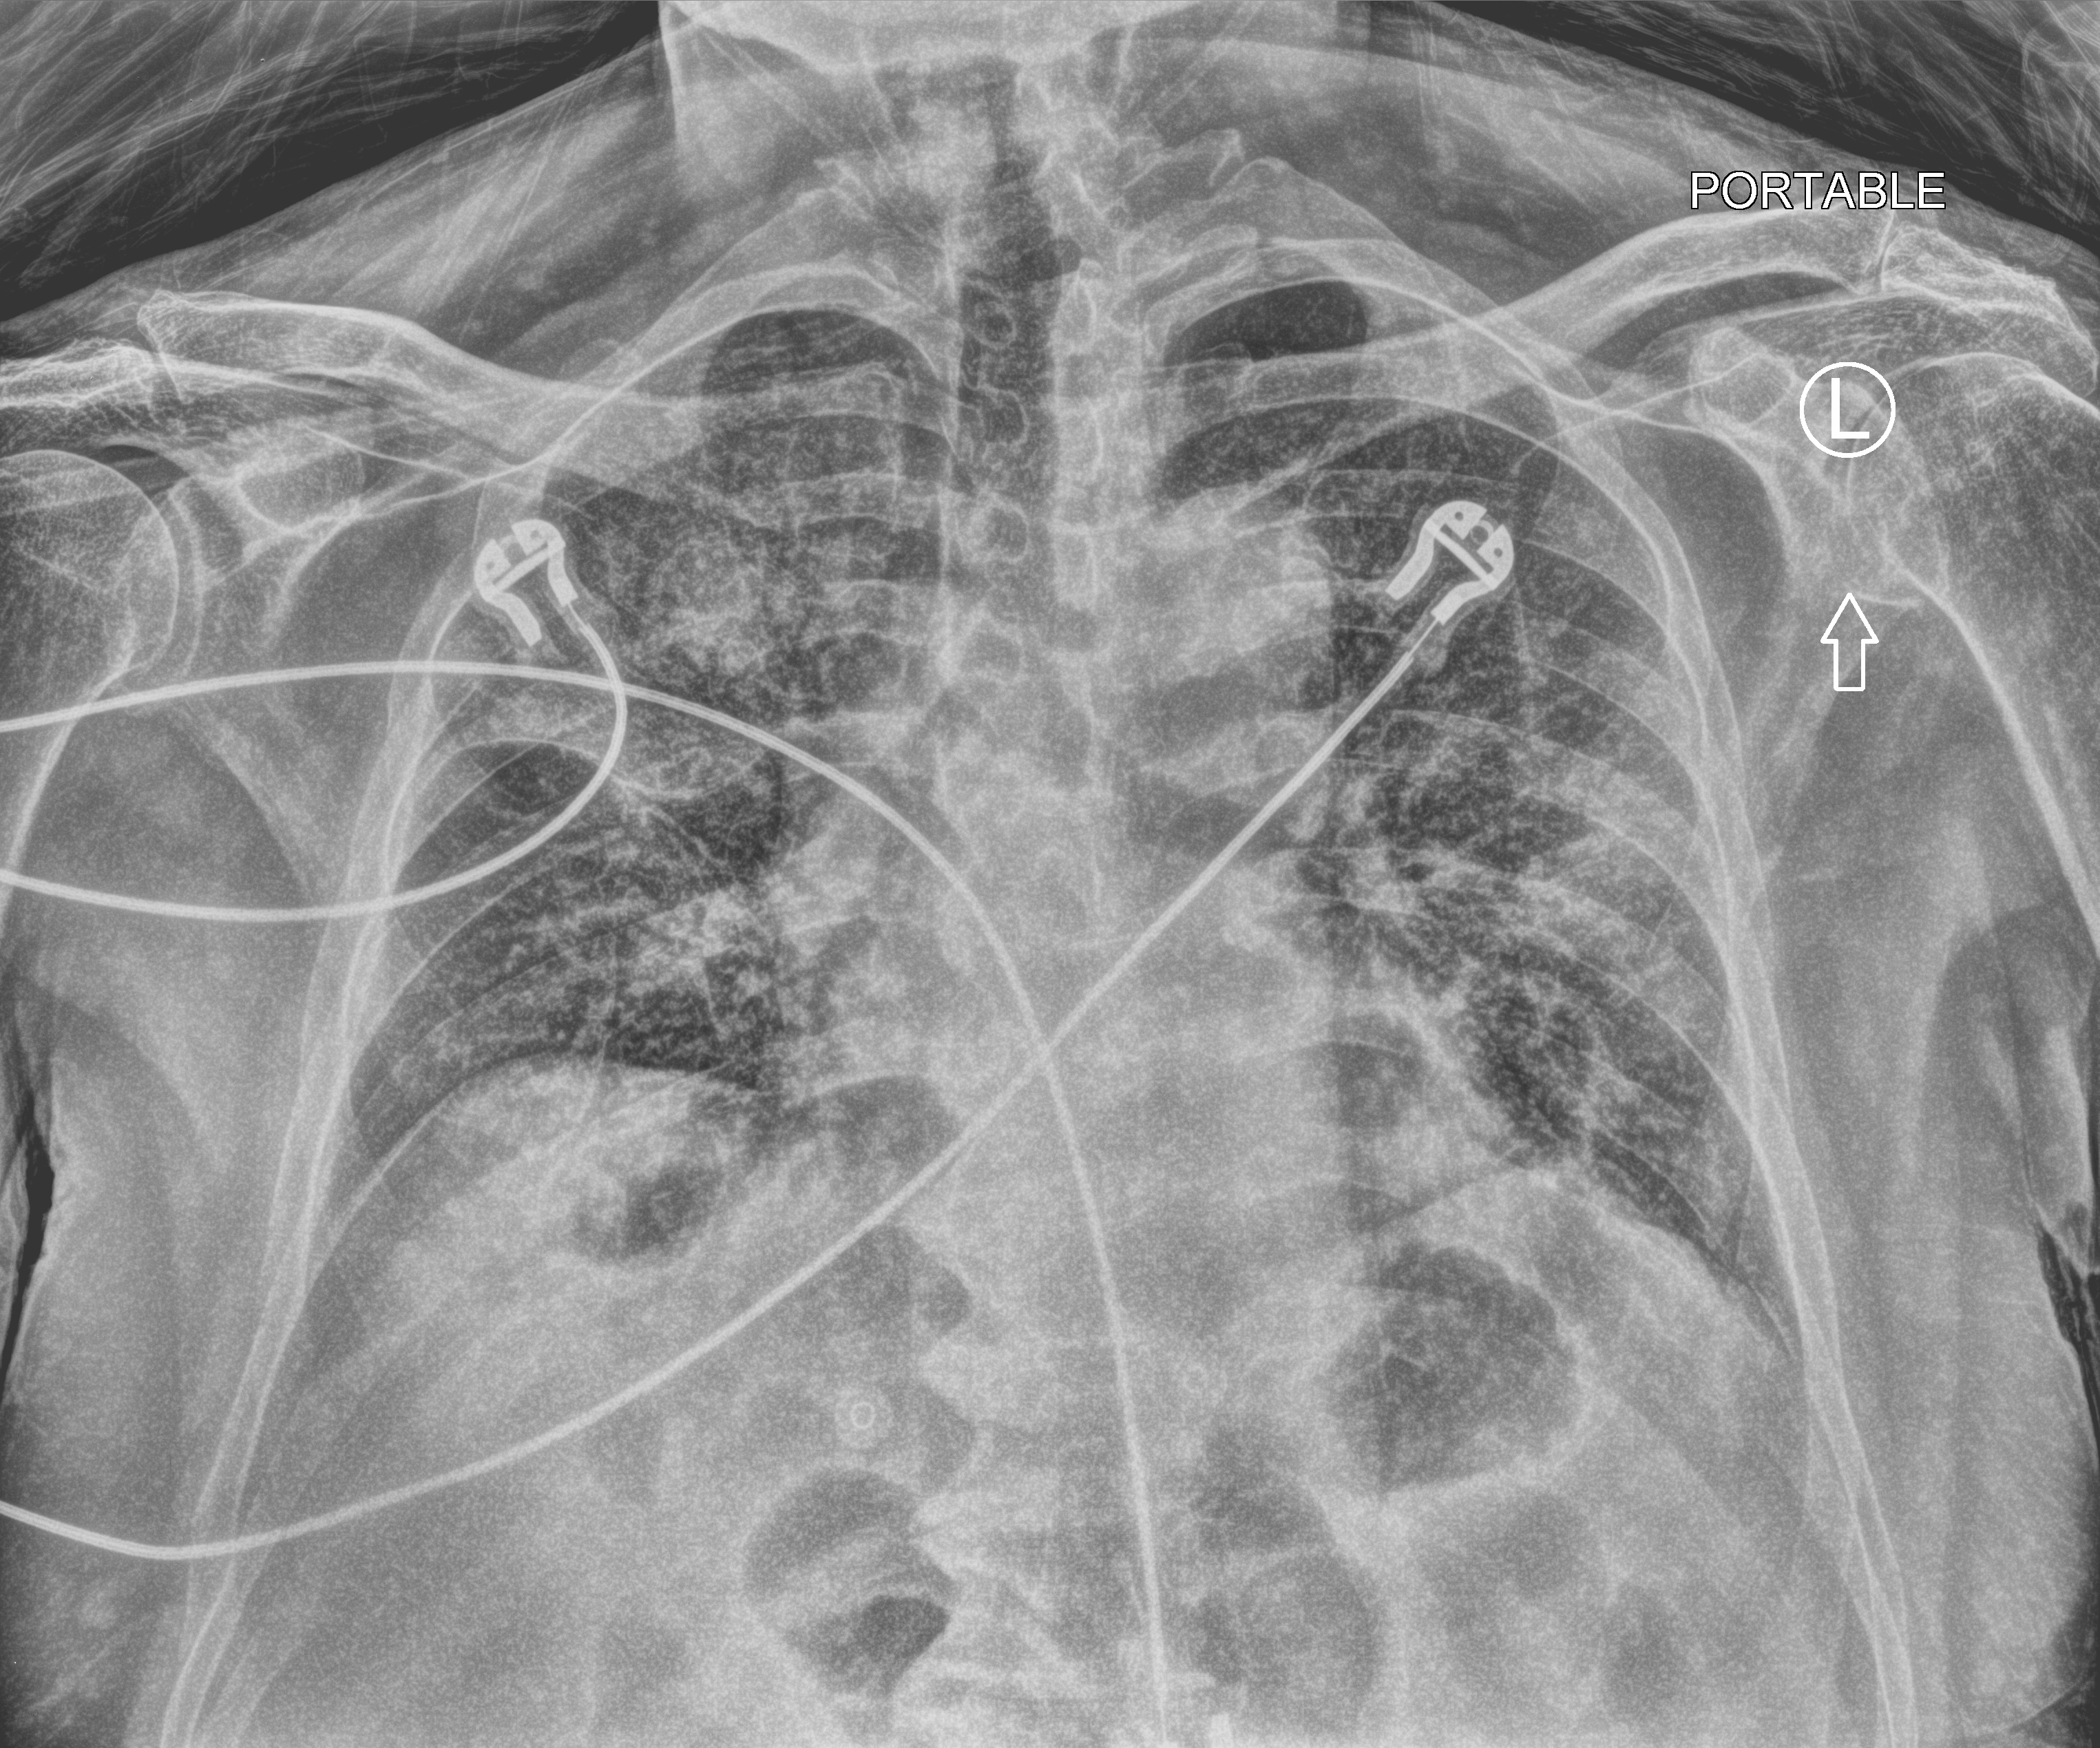
Portable chest radiograph, anteroposterior (AP) projection. Patient hospitalised with COVID-19; male, aged 75–90 years.
From the hospital-stay record, not from the radiograph (when in the stay this image was taken is not recorded): mechanically ventilated during this hospital stay: no.